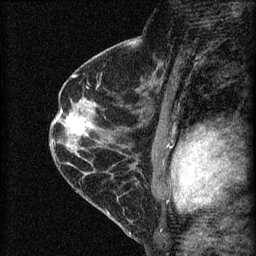
Breast MRI (dynamic contrast-enhanced), one sagittal slice; position 38 of 60 along the scan axis; dynamic contrast-enhanced series, image 2 of 4 at this slice position (ordered by acquisition); 1.5 T; TE 4.2 ms, TR 8.2 ms; 256 × 256 image matrix, field of view 180 × 180 mm. Female patient, age 45 years.
Outlined on this slice (semi-automatic segmentation, software-assisted and operator-edited):
- analysis volume of interest (the breast-tissue region the enhancement analysis was run in; not a lesion): bounding box <58,107,98,147> (left, top, right, bottom; pixels)
- tumour enhancement mask (voxels above the 70 % enhancement threshold inside the analysis volume of interest): <67,114,88,135>